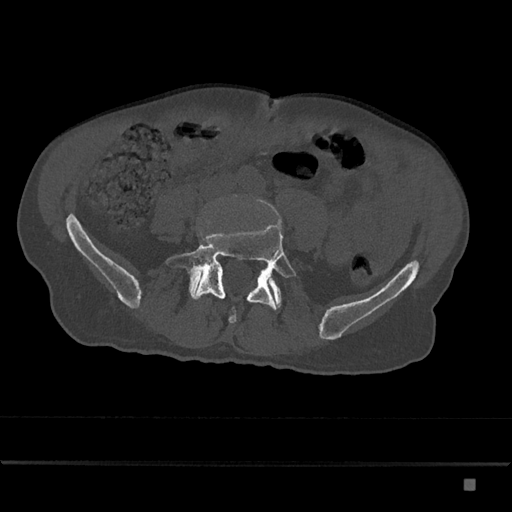
CT including the spine, one axial slice. Position 282 of 797 along the scan axis. Bone window (W 1800 / L 400 HU). 512 × 512 image matrix, field of view 390 × 390 mm. Male patient, age 72 years. Case-level facts recorded for this patient, not image findings: primary cancer: prostate.
Structures marked on this image (semi-automatically segmented with operator editing):
- L5 vertebra: bounding box <166,223,296,324> (left, top, right, bottom; pixels)